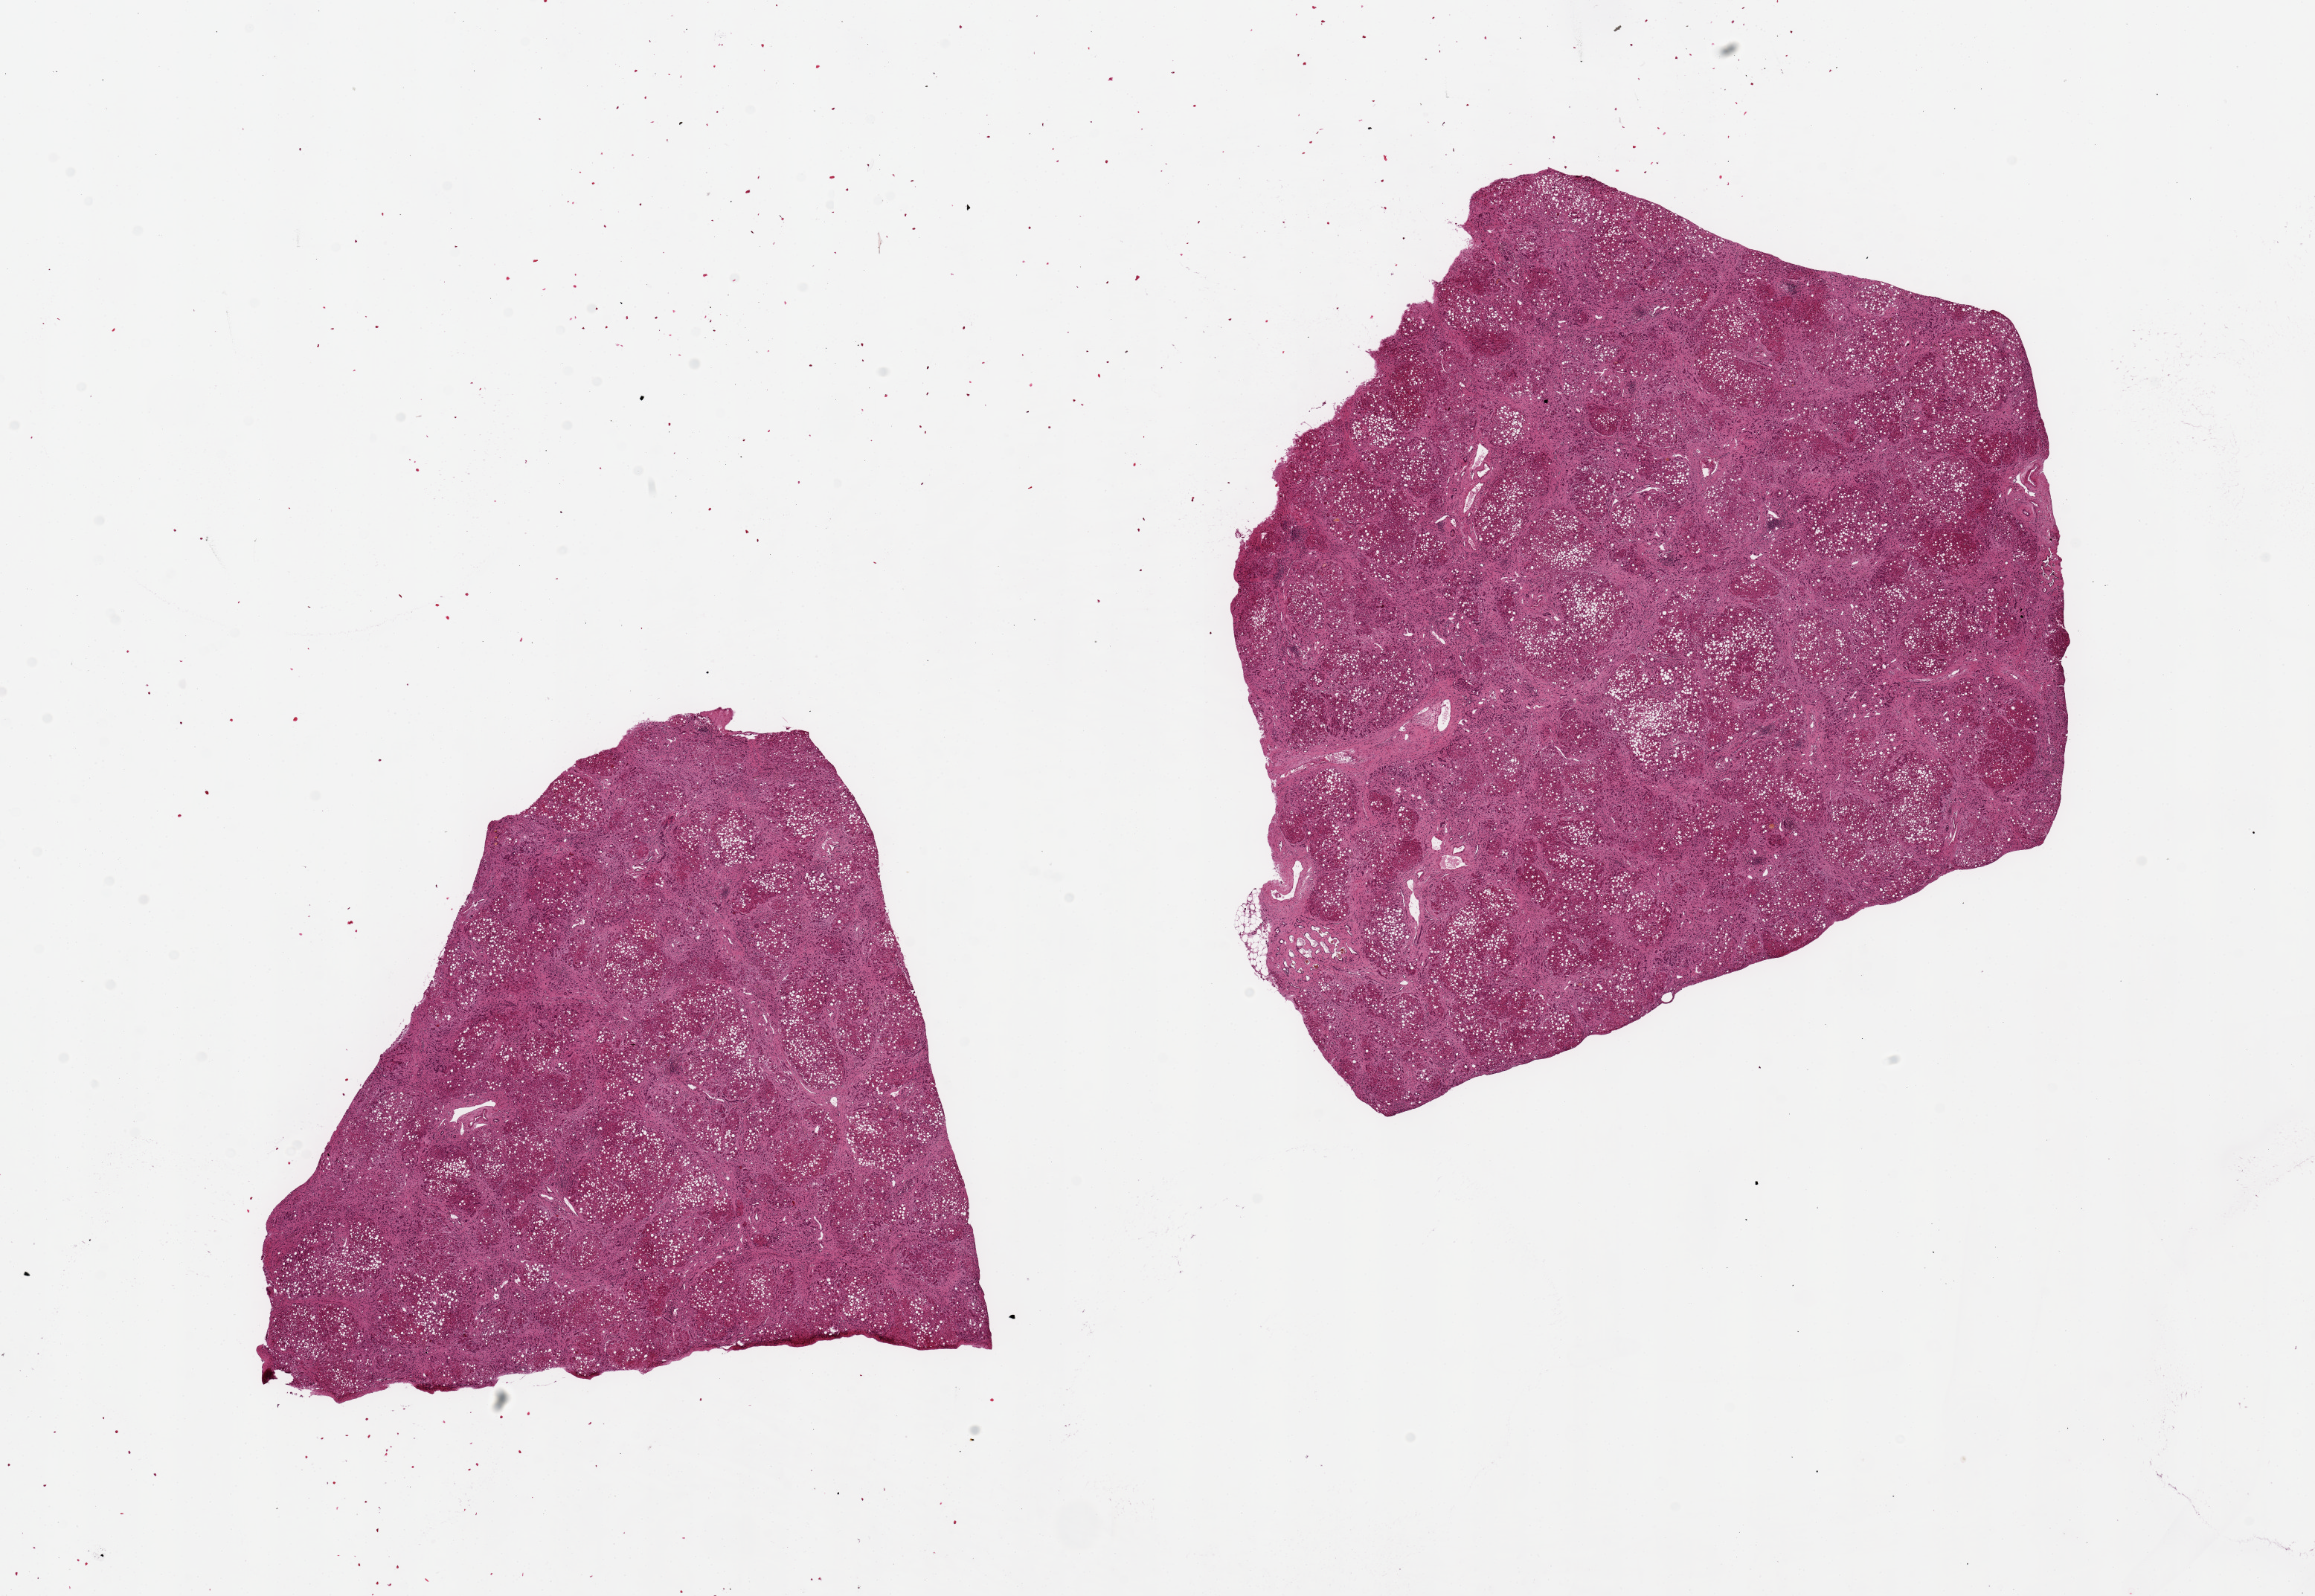
Haematoxylin and eosin whole-slide image, brightfield, a low-resolution overview of the entire scanned area, about 24.6 x 17.0 mm, PAXgene-fixed, paraffin-embedded tissue, section of liver (target tissue), tissue donor sample. Donor sex: female.
Reviewer comment on this tissue sample: 2 pieces, 8x7.5 & 9.5x9mm; cirrhosis with severe macrovesicular steatosis.